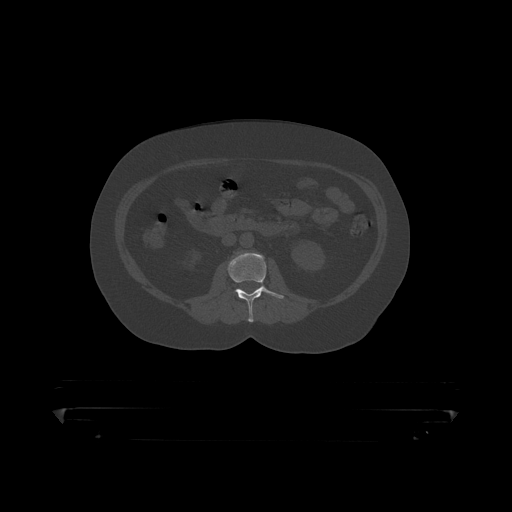
CT including the spine, one axial slice. Slice 113 of 390 in the series (ordered by position). 120 kVp. Bone window (W 1800 / L 400 HU). 512 × 512 image matrix, field of view 650 × 650 mm. Patient: male, 60 years. Case-level facts recorded for this patient, not image findings: primary cancer: prostate.
Outlined on this slice (semi-automatic segmentation, software-assisted and operator-edited):
- L2 vertebra: bounding box (x1, y1, x2, y2) in pixels: (228, 253, 285, 319)